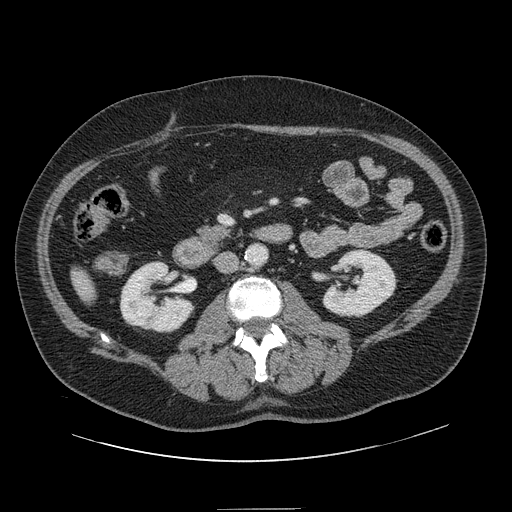
Contrast-enhanced abdominal CT, one axial slice; position 33 of 154 along the scan axis; 120 kVp; intravenous contrast given; soft-tissue window (W 400 / L 40 HU); 2.5 mm slice thickness; 512 × 512 image matrix. Male patient, age 61 years. From the clinical record (not read from this slice): diagnosis: colorectal cancer liver metastases, imaged before liver resection; multiple liver metastases: yes; largest metastasis: 2.6 cm; disease in both lobes: yes.
Structures marked on this image (expert manual segmentation):
- liver: bounding box [x1, y1, x2, y2] px = [73, 271, 94, 299]
- planned liver remnant (the part of the liver to remain after resection): [73, 271, 94, 300]